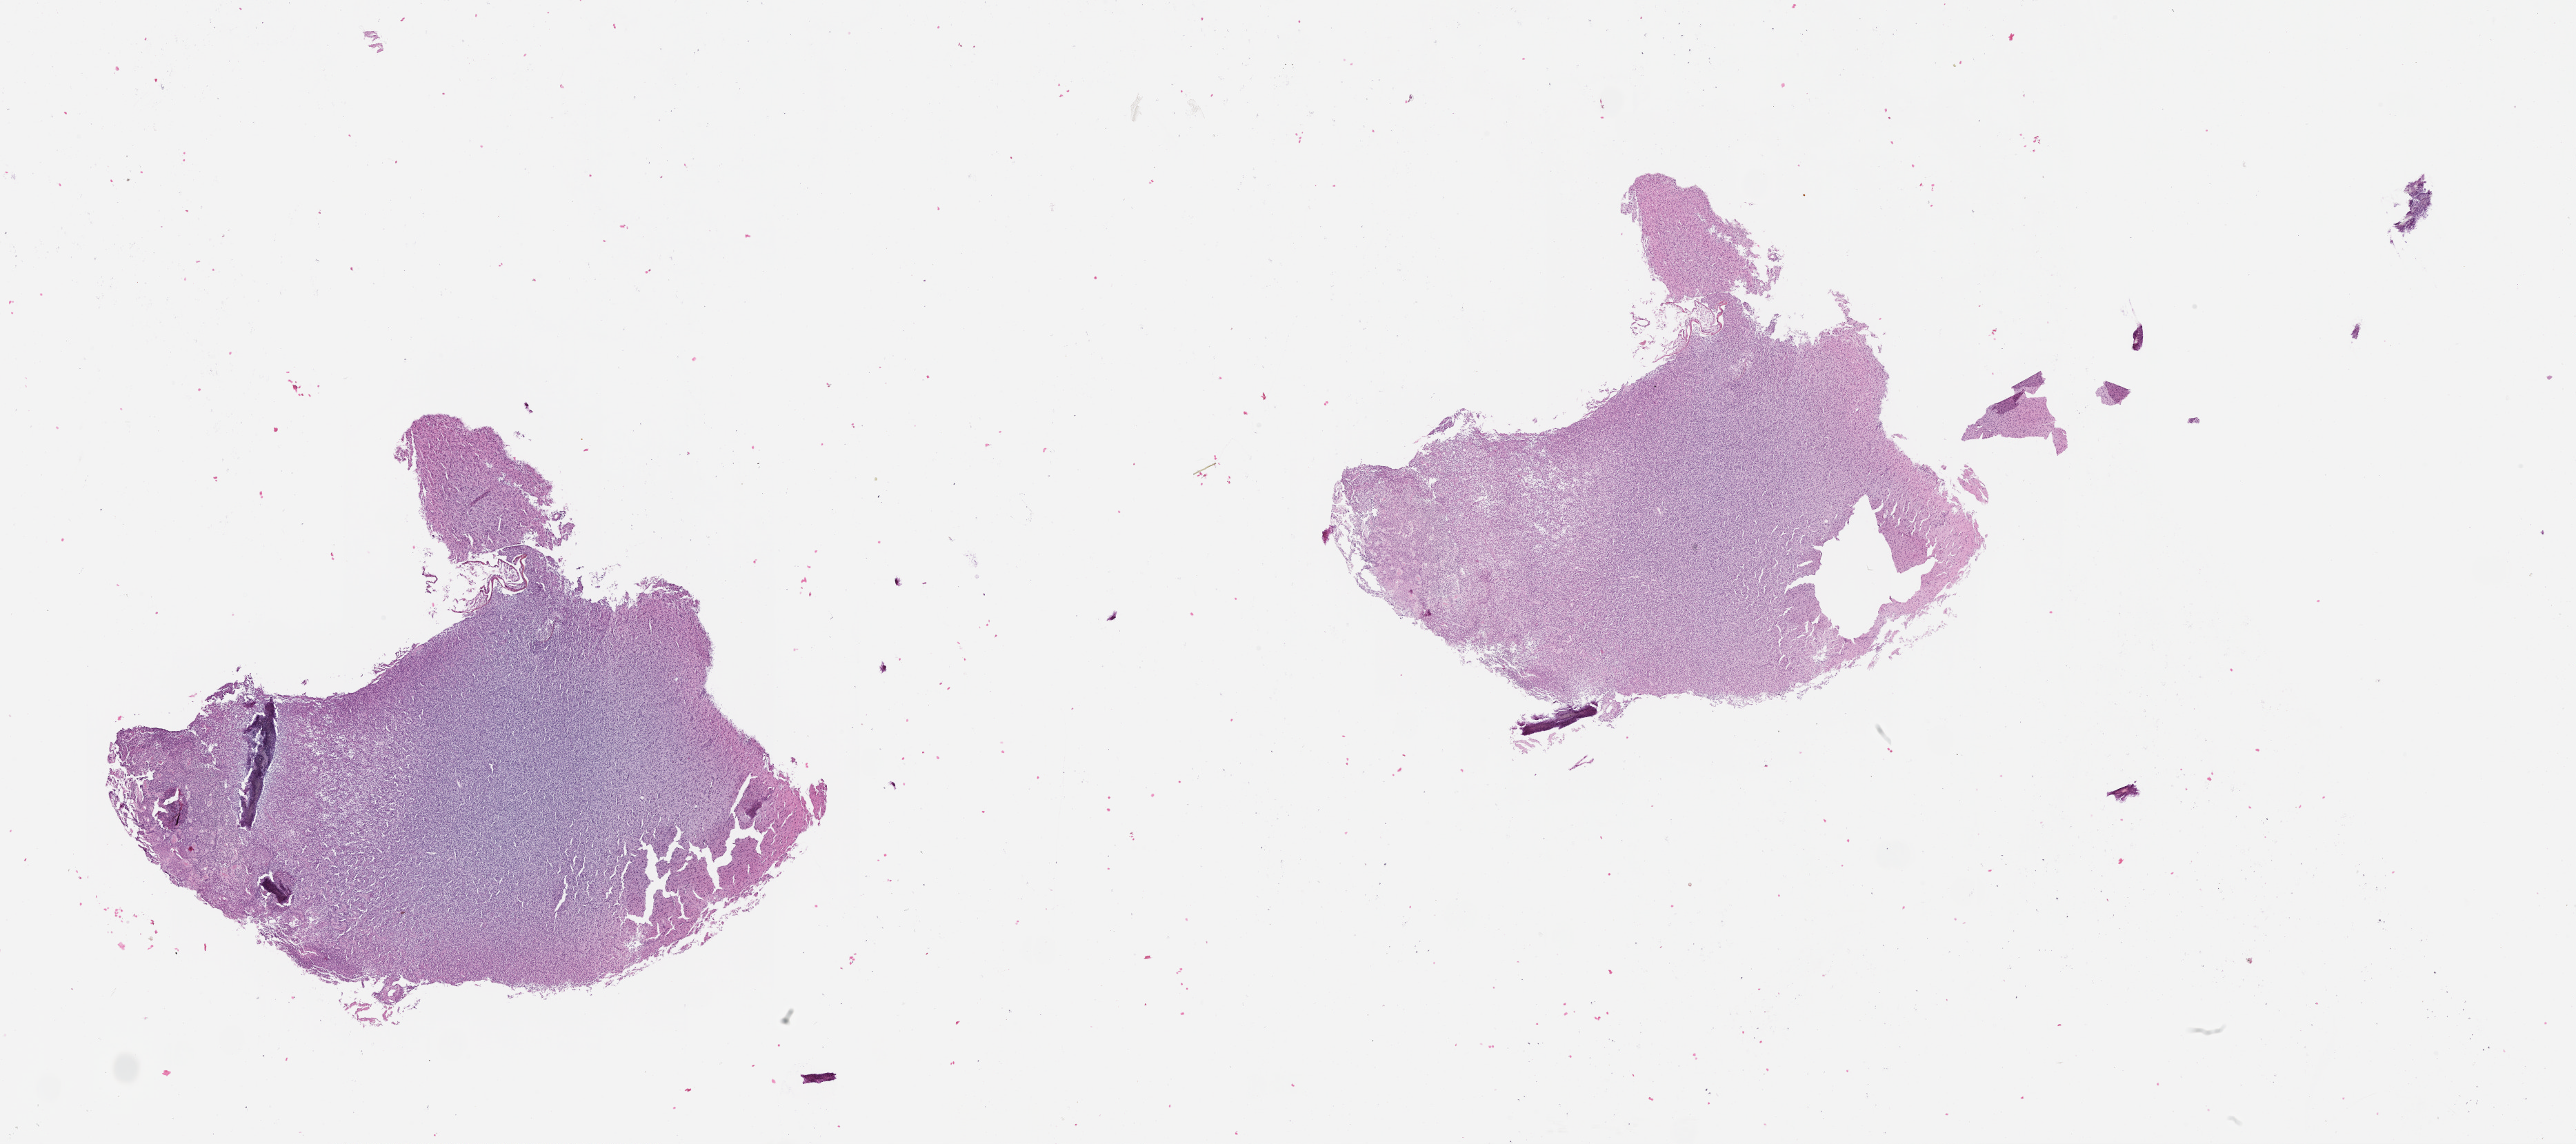
H&E-stained whole-slide image, a low-resolution overview of the entire scanned area, about 30.1 x 13.4 mm. Brain, tumour tissue. 80-year-old female patient.
Diagnosis: Glioblastoma.